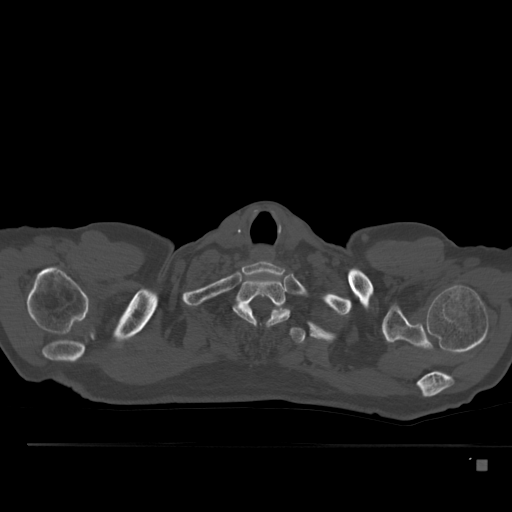
CT including the spine, one axial slice; position 424 of 517 along the scan axis; 120 kVp; bone window (W 1800 / L 400 HU); 1.5 mm slice thickness; 512 × 512 image matrix. Male patient, age 70 years. From the clinical record (not read from this slice): primary cancer: renal; vertebrae with lytic lesions (as recorded): T4, T6, T10, T12, L3, L4, L5.
Annotated regions visible in this slice (semi-automatic segmentation, software-assisted and operator-edited):
- T1 vertebra: bounding box [x1, y1, x2, y2] px = [233, 276, 290, 327]
- T2 vertebra: [241, 303, 306, 344]